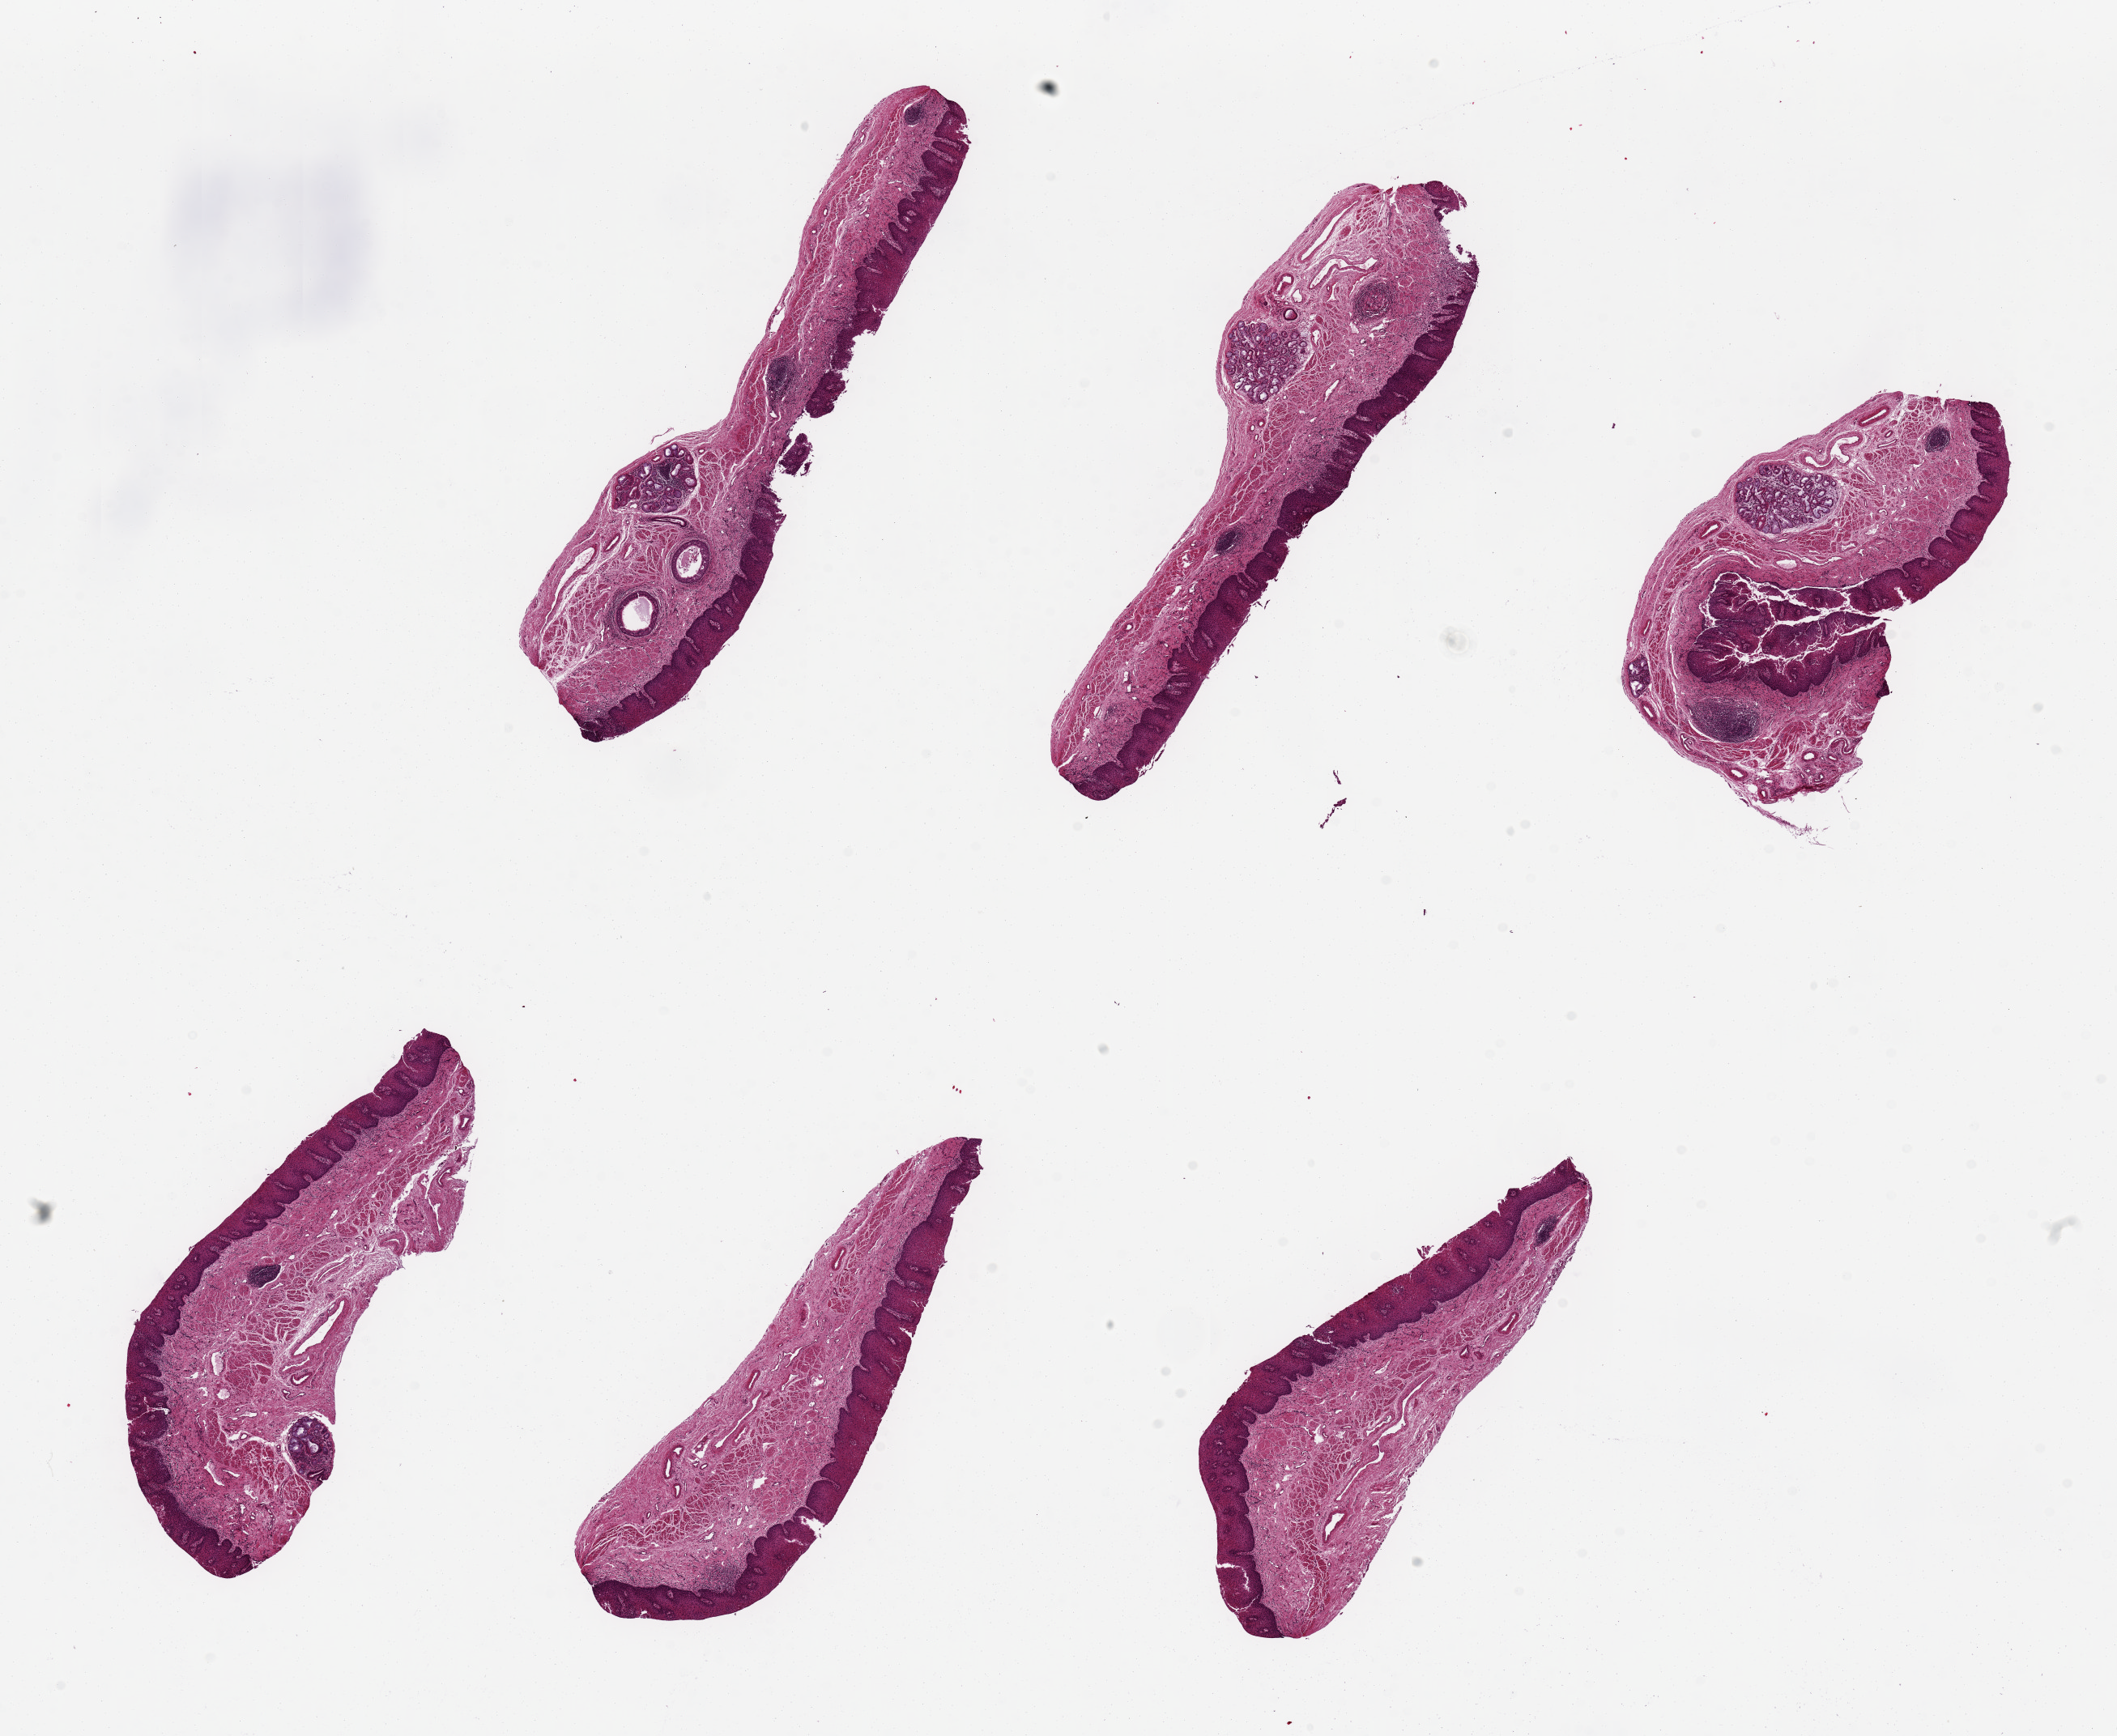
Hematoxylin and eosin (H&E) whole-slide image — low-resolution overview of the scanned area, about 20.7 x 17.0 mm (acquisition: 20x scan); PAXgene-fixed, paraffin-embedded tissue; section of esophageal mucous membrane (target tissue); tissue donor sample. Male donor.
Reviewer comment on this tissue sample: 6 pieces, Squamous mucosa, well-preserved, 15-20% of thickness.